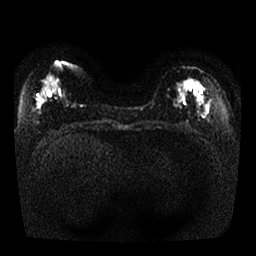
Breast MRI, one axial slice; slice 10 of 25 in the series (ordered by position); diffusion-weighted series; image 2 of 4 stored at this slice position (different b-values; order by instance number); 1.5 T; 4 mm slice thickness; 256 × 256 image matrix. Female patient.
Structures marked on this image (outlined manually by an expert reader):
- tumour on diffusion-weighted imaging: bounding box <179,80,192,93> (left, top, right, bottom; pixels)